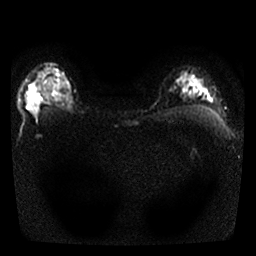
Breast MRI, one axial slice. Position 22 of 25 along the scan axis. Diffusion-weighted series; image 2 of 4 stored at this slice position (different b-values; order by instance number). 1.5 T. 256 × 256 image matrix, field of view 300 × 300 mm. Female patient.
Outlined on this slice (manually delineated by an expert):
- tumour on diffusion-weighted imaging: bounding box (x1, y1, x2, y2) in pixels: (27, 73, 60, 115)